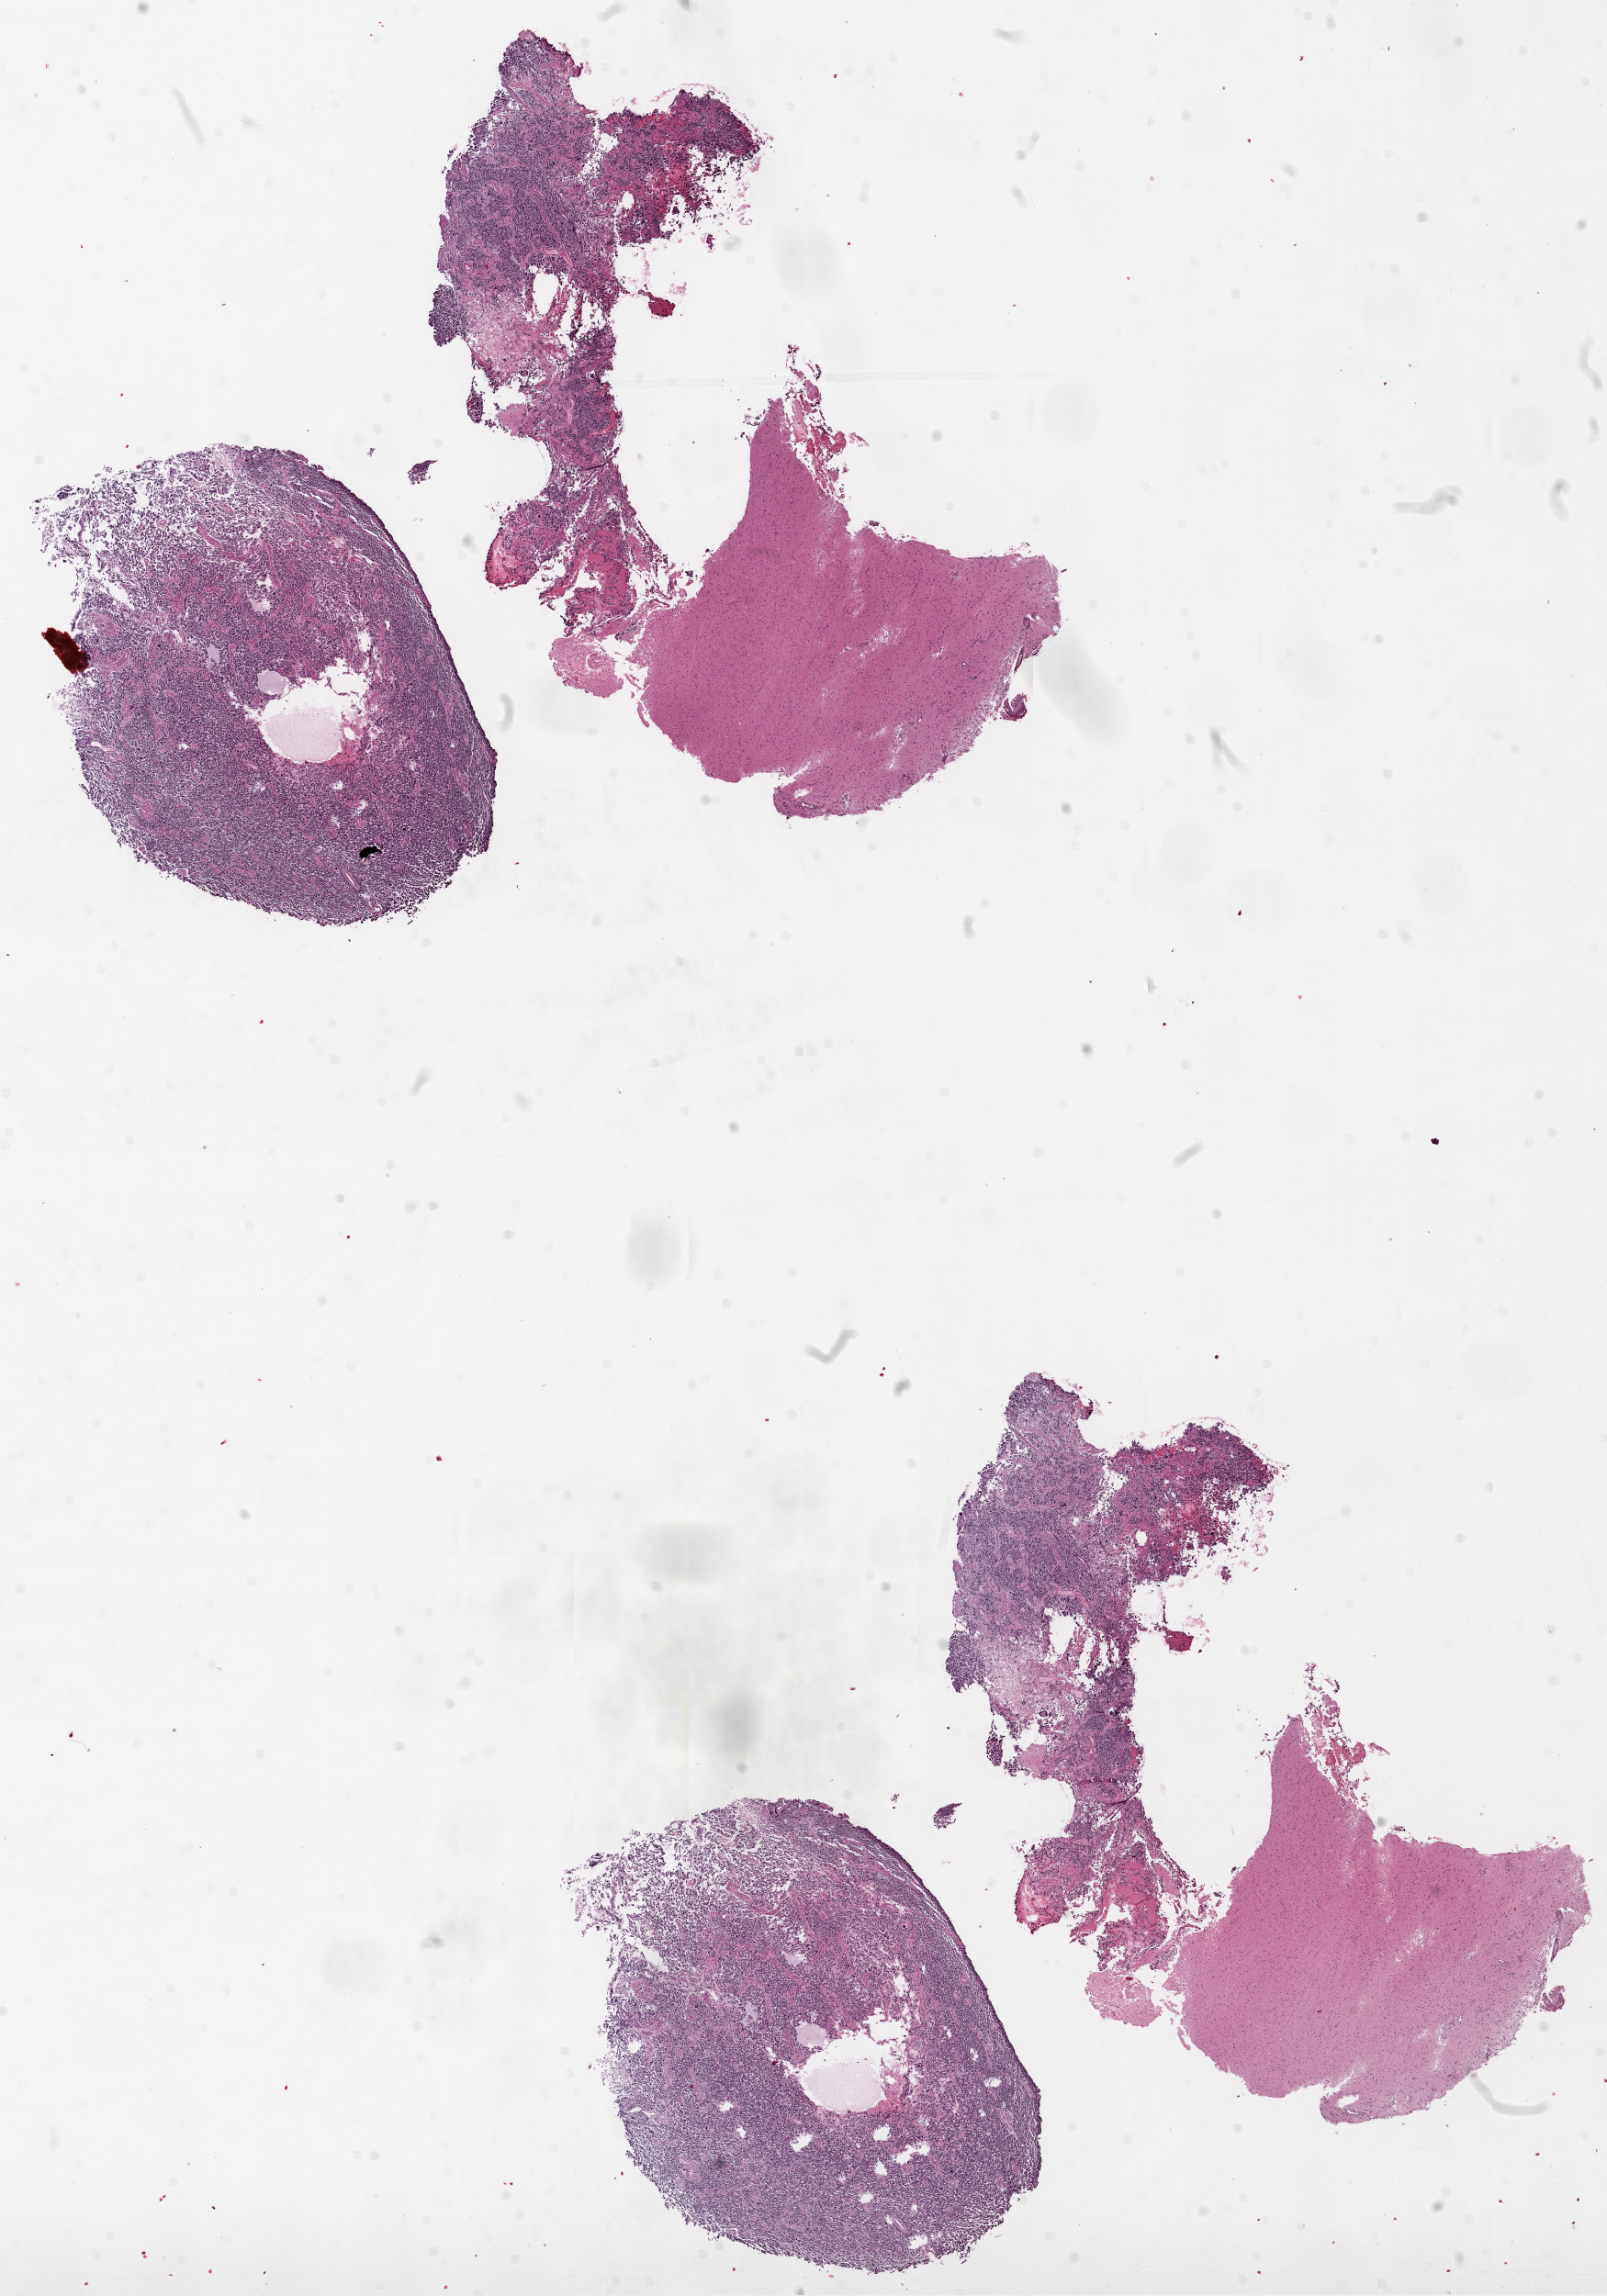
H&E-stained whole-slide image, low-resolution overview of the scanned area, about 14.0 x 20.1 mm; formalin-fixed paraffin-embedded (FFPE) diagnostic section; primary tumour sample from the brain. Male, age 31 years at initial diagnosis.
Diagnosis: Glioblastoma.